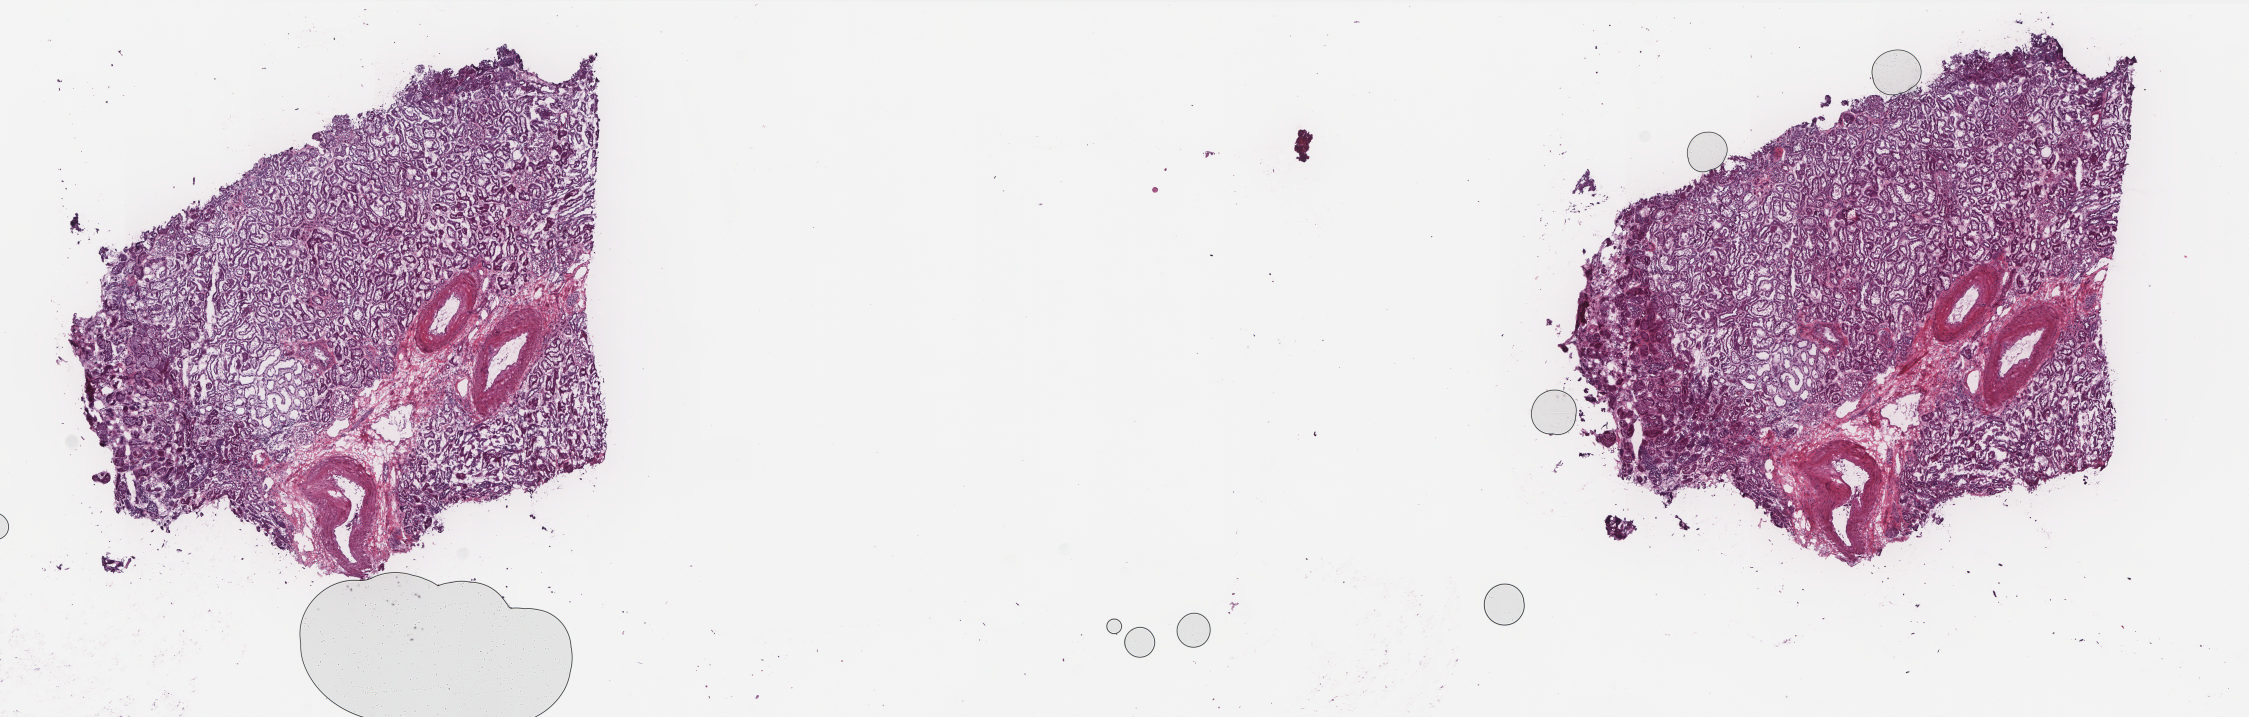
Digitized Hematoxylin and eosin (H&E) stained tissue section (whole slide) — whole scanned area (about 18.0 x 5.7 mm, acquisition: 20x scan) shown as a low-resolution overview. Frozen section from the top of the tissue portion. Sample: solid tissue normal (non-tumour tissue), retroperitoneum and peritoneum. Patient: female, age at initial diagnosis 61 years. Composition of this section per pathologist review: tumour cells 0%, tumour nuclei 0%, normal cells 80%, stromal cells 20%, necrosis 0%. Infiltration values recorded for this section: lymphocyte infiltration 0%, monocyte infiltration 0%, neutrophil infiltration 0%.
This section: solid tissue normal (non-tumour) sample from the same patient. Patient diagnosis: Dedifferentiated liposarcoma.